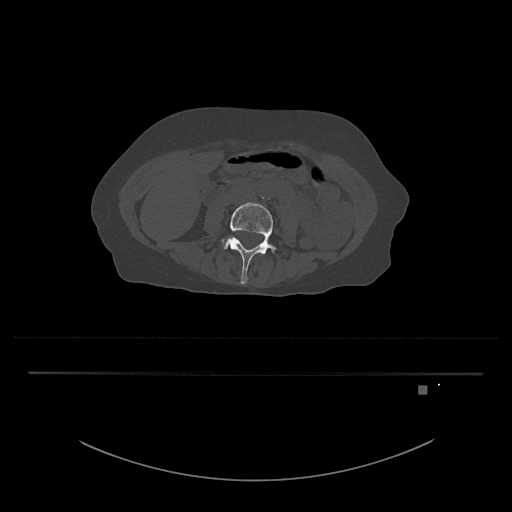
CT including the spine, one axial slice. Position 362 of 797 along the scan axis. Bone window (W 1800 / L 400 HU). 0.5 mm slice thickness. 512 × 512 image matrix, field of view 500 × 500 mm. Female patient, age 57 years. Case-level facts recorded for this patient, not image findings: primary cancer: cervical.
Structures marked on this image (semi-automatically segmented with operator editing):
- L4 vertebra: bounding box (x1, y1, x2, y2) in pixels: (221, 202, 277, 284)